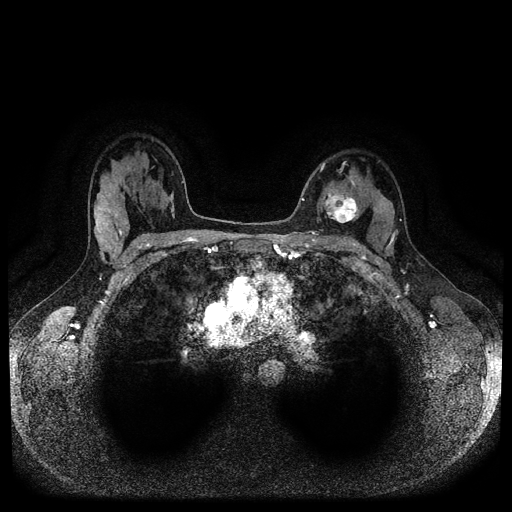
Breast MRI (dynamic contrast-enhanced, multi-phase), one axial slice; slice 68 of 116 in the series (ordered by position); dynamic contrast-enhanced series, time point 2 of 5 at this slice position (early post-contrast); 1.5 T; TE 2.6 ms, TR 5.3 ms; 512 × 512 image matrix, field of view 350 × 350 mm. Patient: female, 33 years.
Structures marked on this image (semi-automatic segmentation, software-assisted and operator-edited):
- breast lesion (labelled 'tumour' in the annotation; benign lesions carry a separate 'benign' label): box from (x=323, y=186) to (x=359, y=223) px